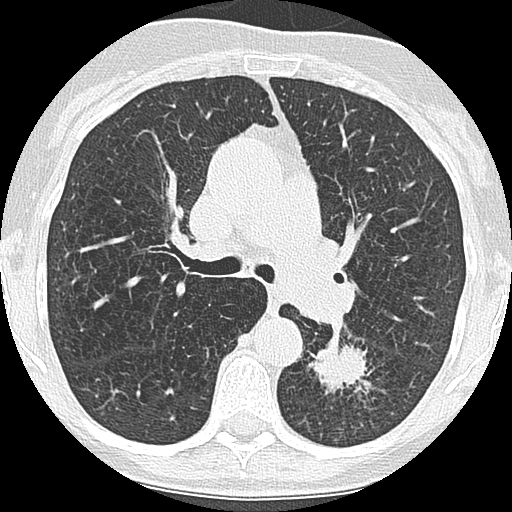
Low-dose screening chest CT, one axial slice. Position 111 of 171 along the scan axis. Reconstruction kernel LUNG. Lung window (W 1500 / L -600 HU). 2.5 mm slice thickness. 512 × 512 image matrix, field of view 280 × 280 mm.
Outlined on this slice (expert manual segmentation):
- lesion 1 (tumor, lower lobe of left lung): bounding box (x1, y1, x2, y2) in pixels: (308, 342, 367, 394)